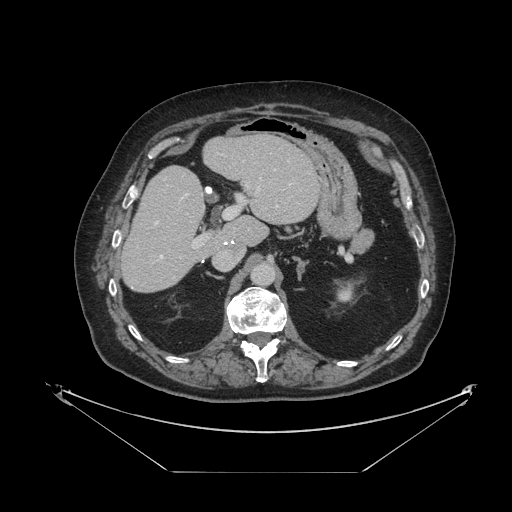
Contrast-enhanced abdominal CT, one axial slice. Position 61 of 121 along the scan axis. Reconstruction kernel STANDARD. Intravenous contrast given. Soft-tissue window (W 400 / L 40 HU). 2.5 mm slice thickness. 512 × 512 image matrix. Male patient, age 68 years. Case-level facts recorded for this patient, not image findings: diagnosis: colorectal cancer liver metastases, imaged before liver resection; multiple liver metastases: no; largest metastasis: 4 cm.
Annotated regions visible in this slice (manually delineated by an expert):
- hepatic veins: box from (x=160, y=184) to (x=291, y=259) px
- liver: (x=122, y=136)–(x=320, y=292)
- planned liver remnant (the part of the liver to remain after resection): (x=122, y=136)–(x=320, y=292)
- portal vein (with intrahepatic branches): (x=192, y=179)–(x=261, y=248)